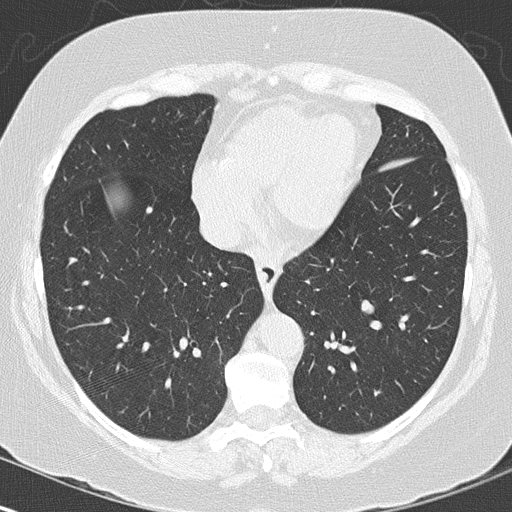
Low-dose screening chest CT, one axial slice; position 50 of 144 along the scan axis; 120 kVp; lung window (W 1500 / L -600 HU); 512 × 512 image matrix, field of view 316 × 316 mm.
Annotated regions visible in this slice (manually delineated by an expert):
- lesion 1 (tumor, lower lobe of left lung): bounding box (x1, y1, x2, y2) in pixels: (361, 300, 374, 314)